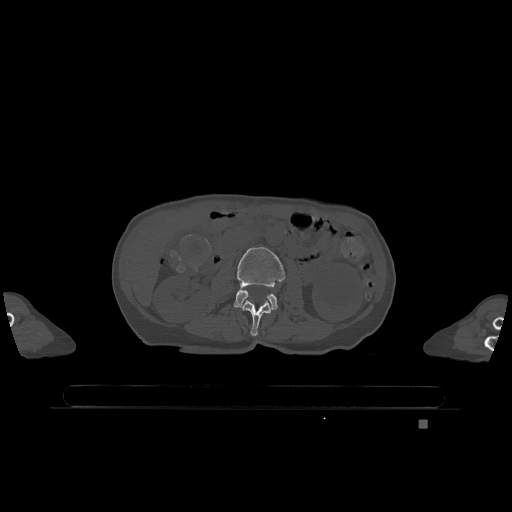
CT including the spine, one axial slice. Slice 383 of 1317 in the series (ordered by position). Bone window (W 1800 / L 400 HU). 0.5 mm slice thickness. 512 × 512 image matrix, field of view 500 × 500 mm. Female patient, age 74 years. Case-level facts recorded for this patient, not image findings: primary cancer: lung; vertebrae with lytic lesions (as recorded): T1, T4, T5, T6, L4, L5.
Structures marked on this image (semi-automatic segmentation, software-assisted and operator-edited):
- L2 vertebra: bounding box (x1, y1, x2, y2) in pixels: (242, 300, 271, 336)
- L3 vertebra: (234, 247, 286, 310)